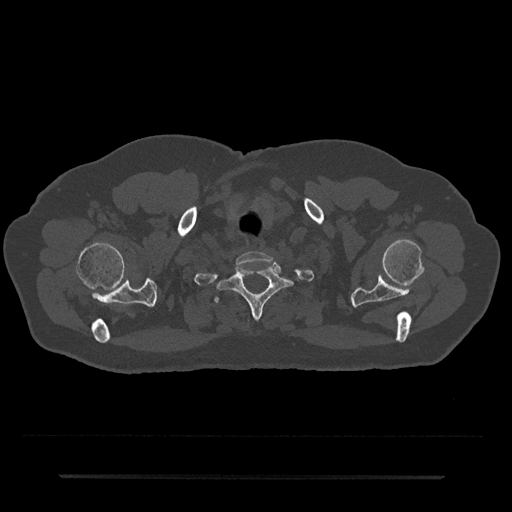
CT including the spine, one axial slice; position 642 of 797 along the scan axis; 120 kVp; bone window (W 1800 / L 400 HU); 512 × 512 image matrix, field of view 437 × 437 mm. Patient: male, 69 years. Case-level facts recorded for this patient, not image findings: primary cancer: prostate.
Annotated regions visible in this slice (semi-automatic segmentation, software-assisted and operator-edited):
- T1 vertebra: bounding box <217,264,300,319> (left, top, right, bottom; pixels)
- T2 vertebra: <214,297,219,303>